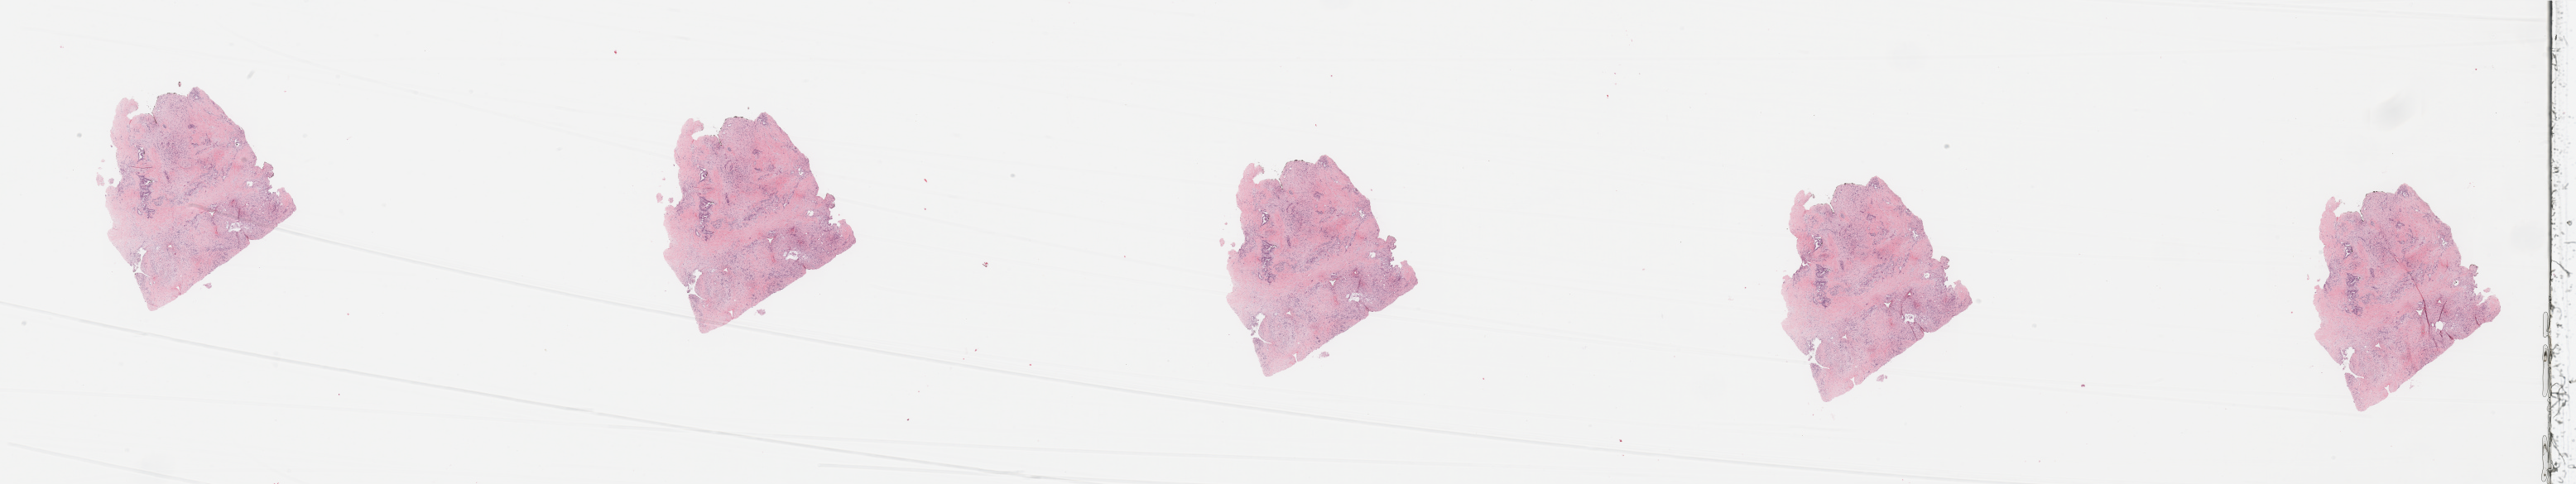
Digitized Hematoxylin and eosin (H&E) stained tissue section (whole slide) — shown as a low-resolution overview of the whole scanned area (about 49.2 x 9.3 mm). Tumour tissue sample, sampled site: pancreas. Patient: male, age 77 years. Histologic grade: G2 (moderately differentiated). Pathologist review of this section (percent, as recorded): tumour nuclei 20%, necrosis 0%.
Primary tumour site (as recorded): head. AJCC pathologic stage: III. Diagnosis: Infiltrating duct carcinoma, NOS.